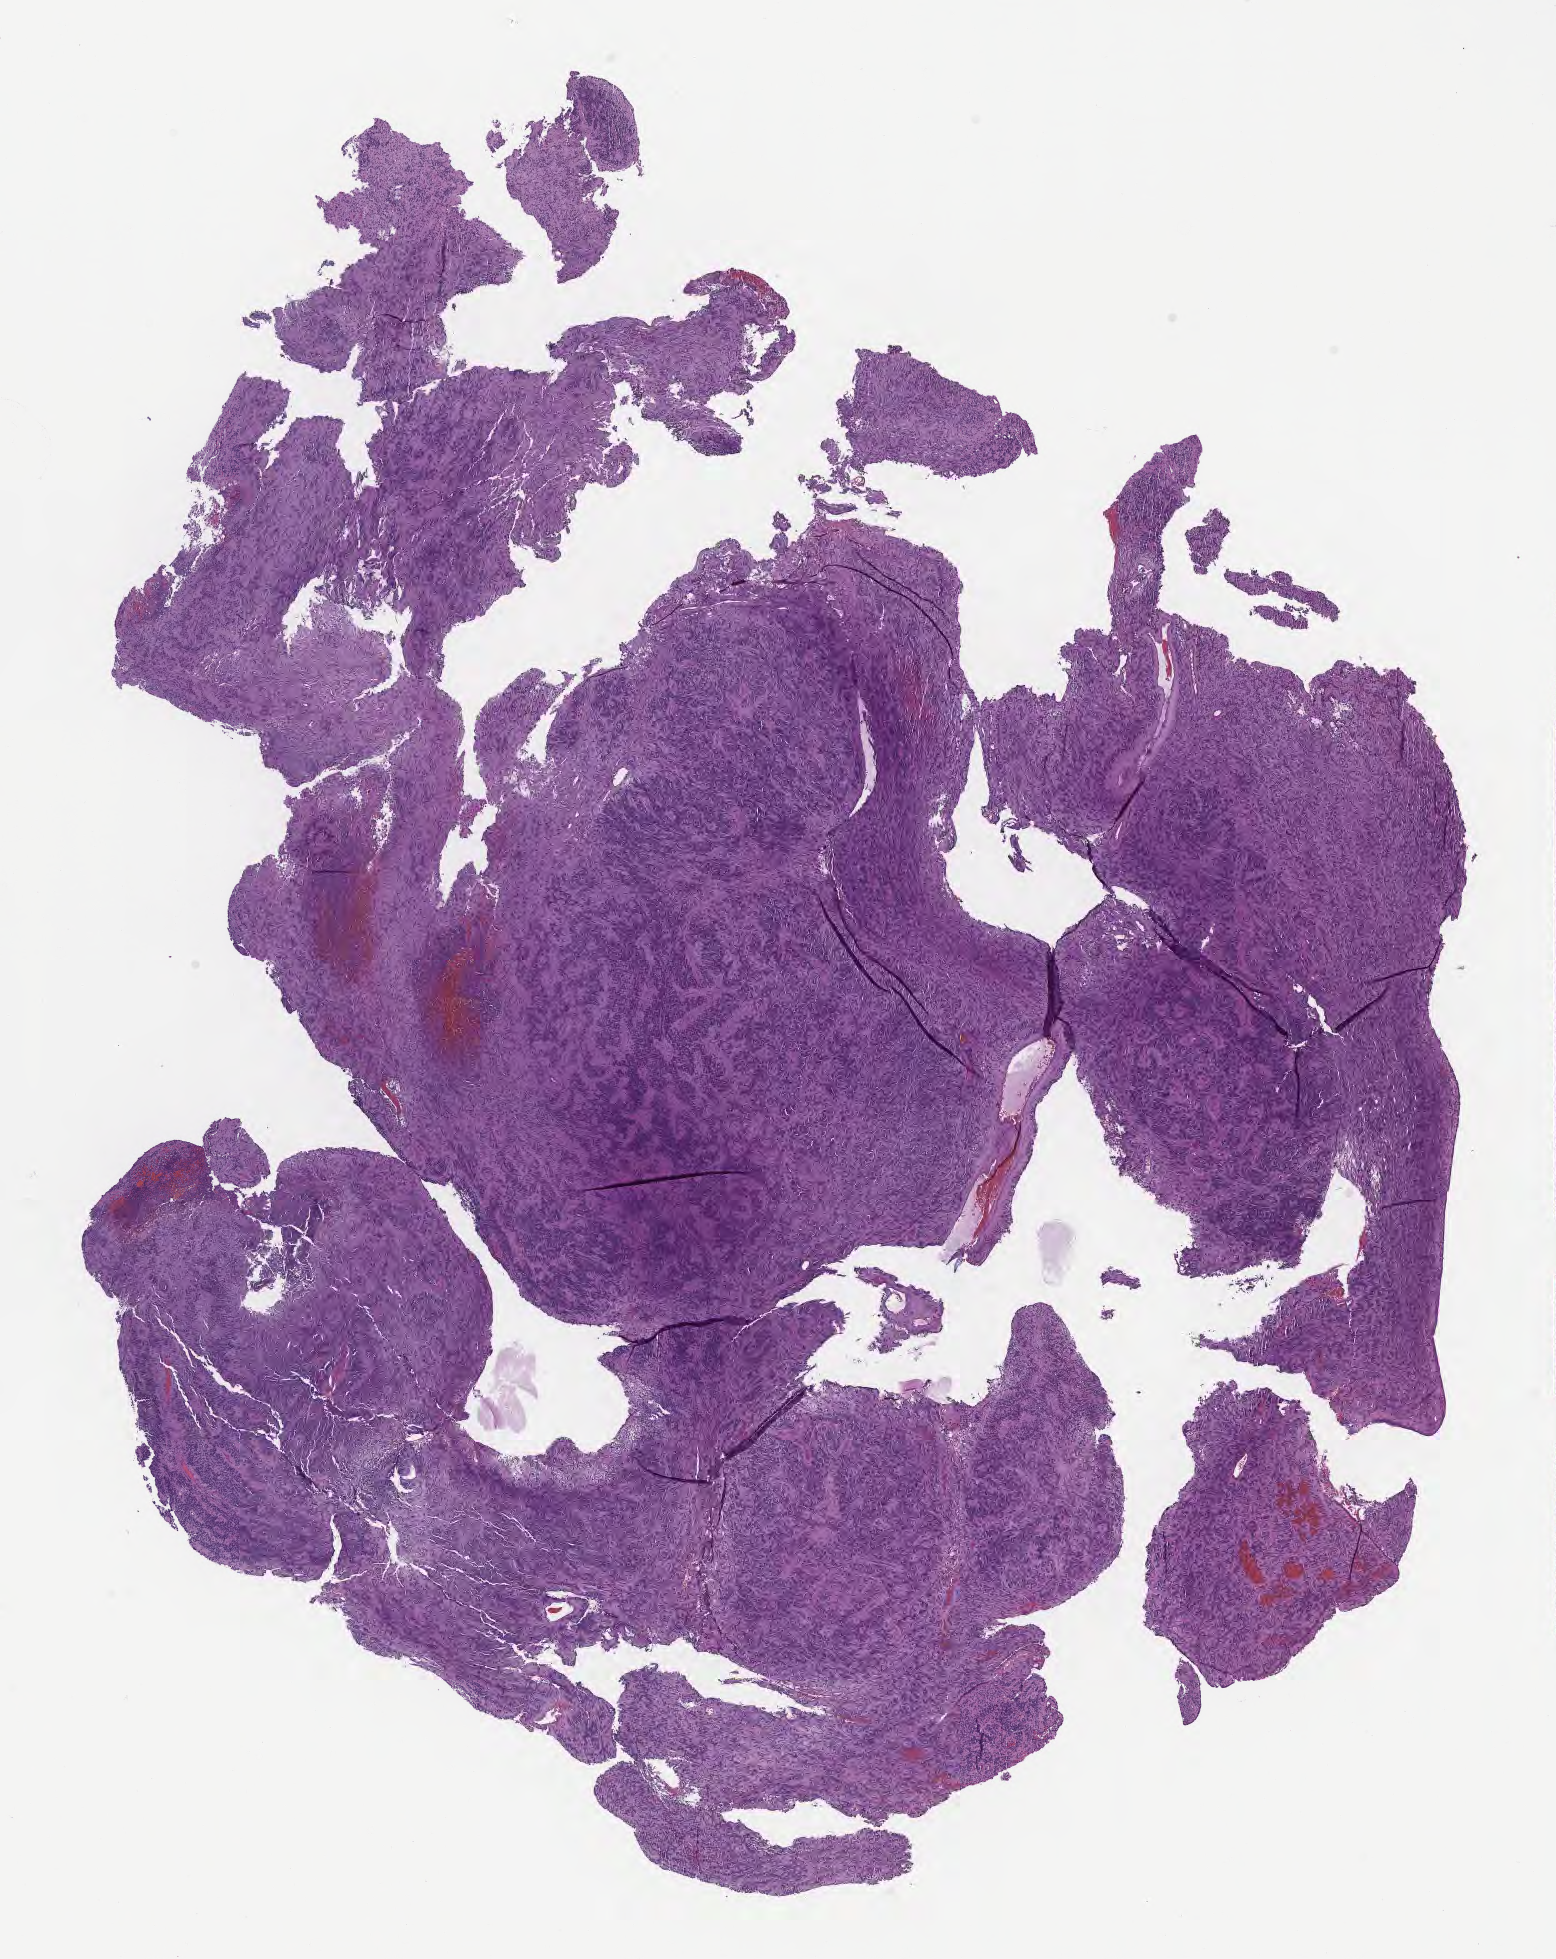
H&E whole-slide image of tumor tissue from the brain, low-resolution overview of the scanned area, about 12.6 x 15.8 mm, formalin-fixed paraffin-embedded section. Female patient, age 34 months.
Recorded diagnosis: Ependymoma, NOS.